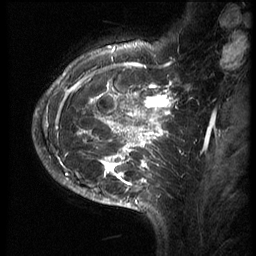
Breast MRI (dynamic contrast-enhanced), one sagittal slice. Position 20 of 70 along the scan axis. 3 images stored at this slice position (order not interpretable as contrast timing). 1.5 T. TE 4.2 ms, TR 9 ms. 2.5 mm slice thickness. 256 × 256 image matrix, field of view 180 × 180 mm. Female patient, age 28 years. Case-level facts recorded for this patient, not image findings: setting: breast cancer imaged before/during neoadjuvant chemotherapy.
Structures marked on this image (semi-automatically segmented with operator editing):
- analysis volume of interest (the breast-tissue region the enhancement analysis was run in; not a lesion): bounding box [x1, y1, x2, y2] px = [43, 42, 186, 215]
- tumour enhancement mask (voxels above the 140 % enhancement threshold inside the analysis volume of interest): [56, 47, 179, 202]